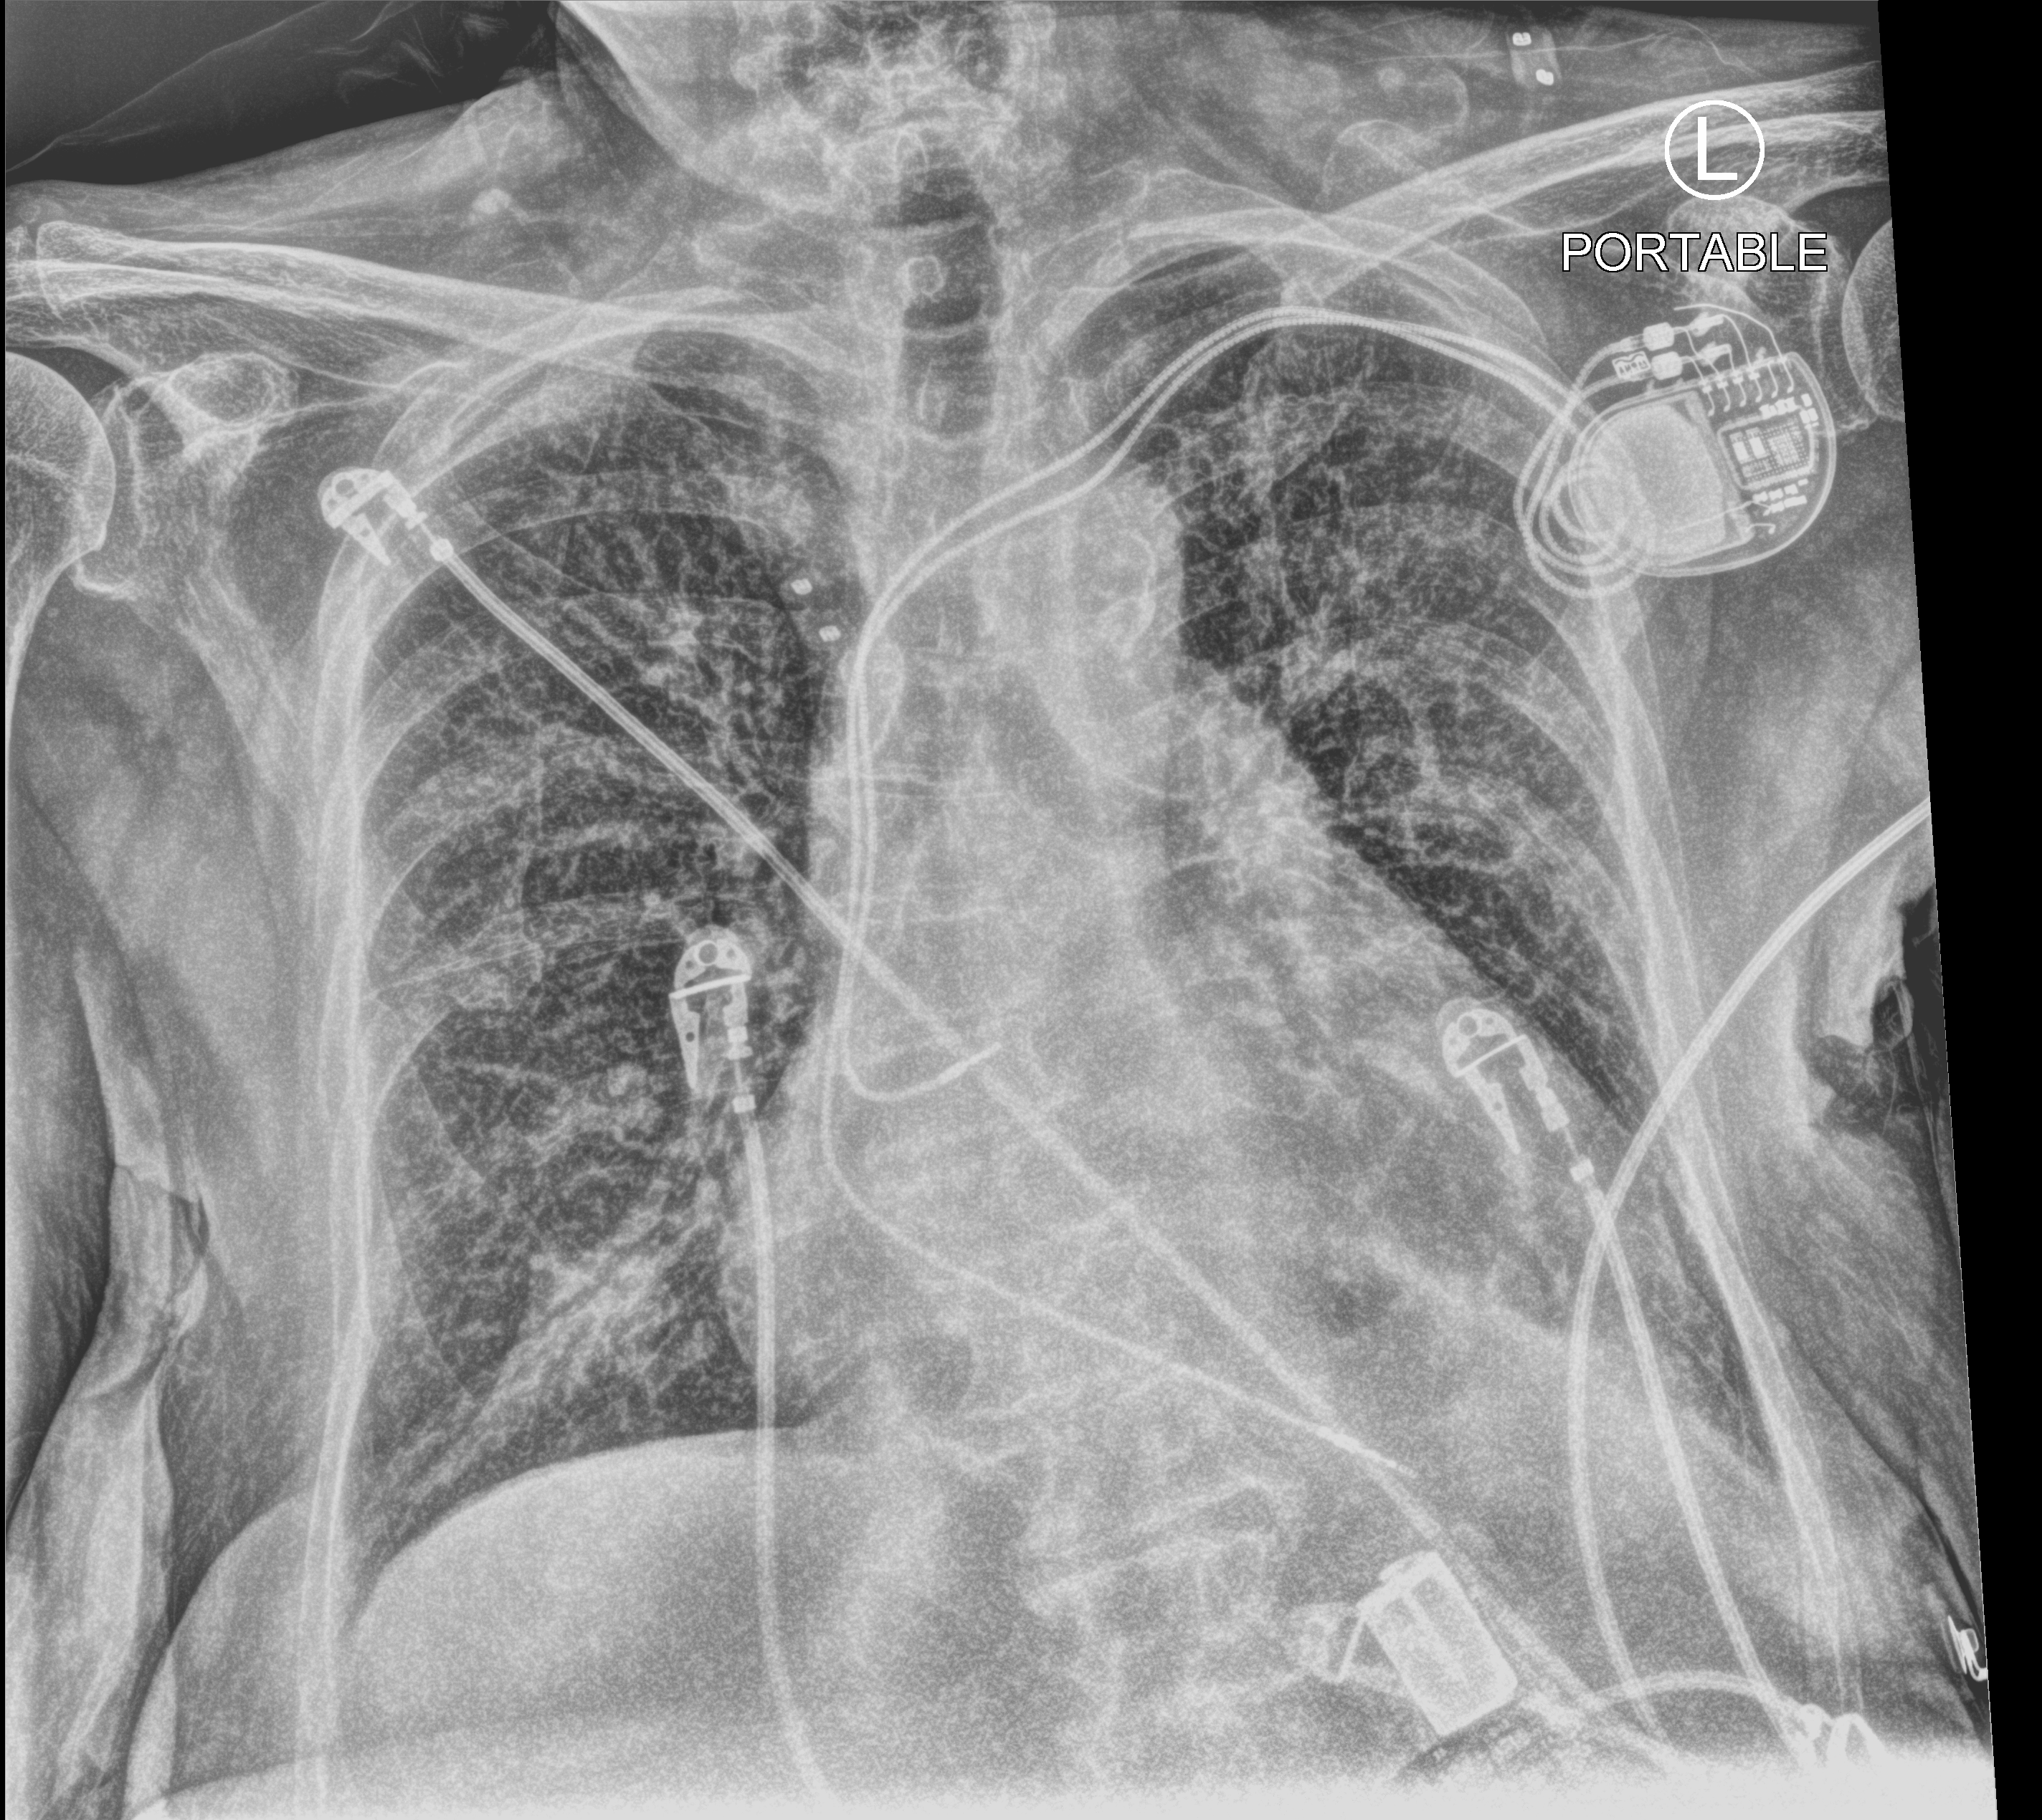
Portable chest radiograph, anteroposterior (AP) projection. Female patient hospitalised with COVID-19, age 75–90 years.
From the hospital-stay record, not from the radiograph (when in the stay this image was taken is not recorded):
- mechanically ventilated during this hospital stay: no
- admitted to intensive care during this hospital stay: no
- length of hospital stay: 13 days